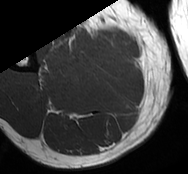
MRI of an extremity soft-tissue mass, one axial slice. Slice 19 of 93 in the series (ordered by position). MR volume resampled by the dataset authors to the PET/CT grid (not the native acquisition matrix). 188 × 174 image matrix, field of view 184 × 170 mm. Male patient. Case-level facts recorded for this patient, not image findings: histological type: undifferentiated - pleiomorphic; grade: high; site of the primary tumour: right thigh.
Annotated regions visible in this slice (expert contour drawn on MRI and transferred to this co-registered scan by the dataset authors):
- gross tumour volume including surrounding oedema: bounding box (x1, y1, x2, y2) in pixels: (54, 42, 82, 66)